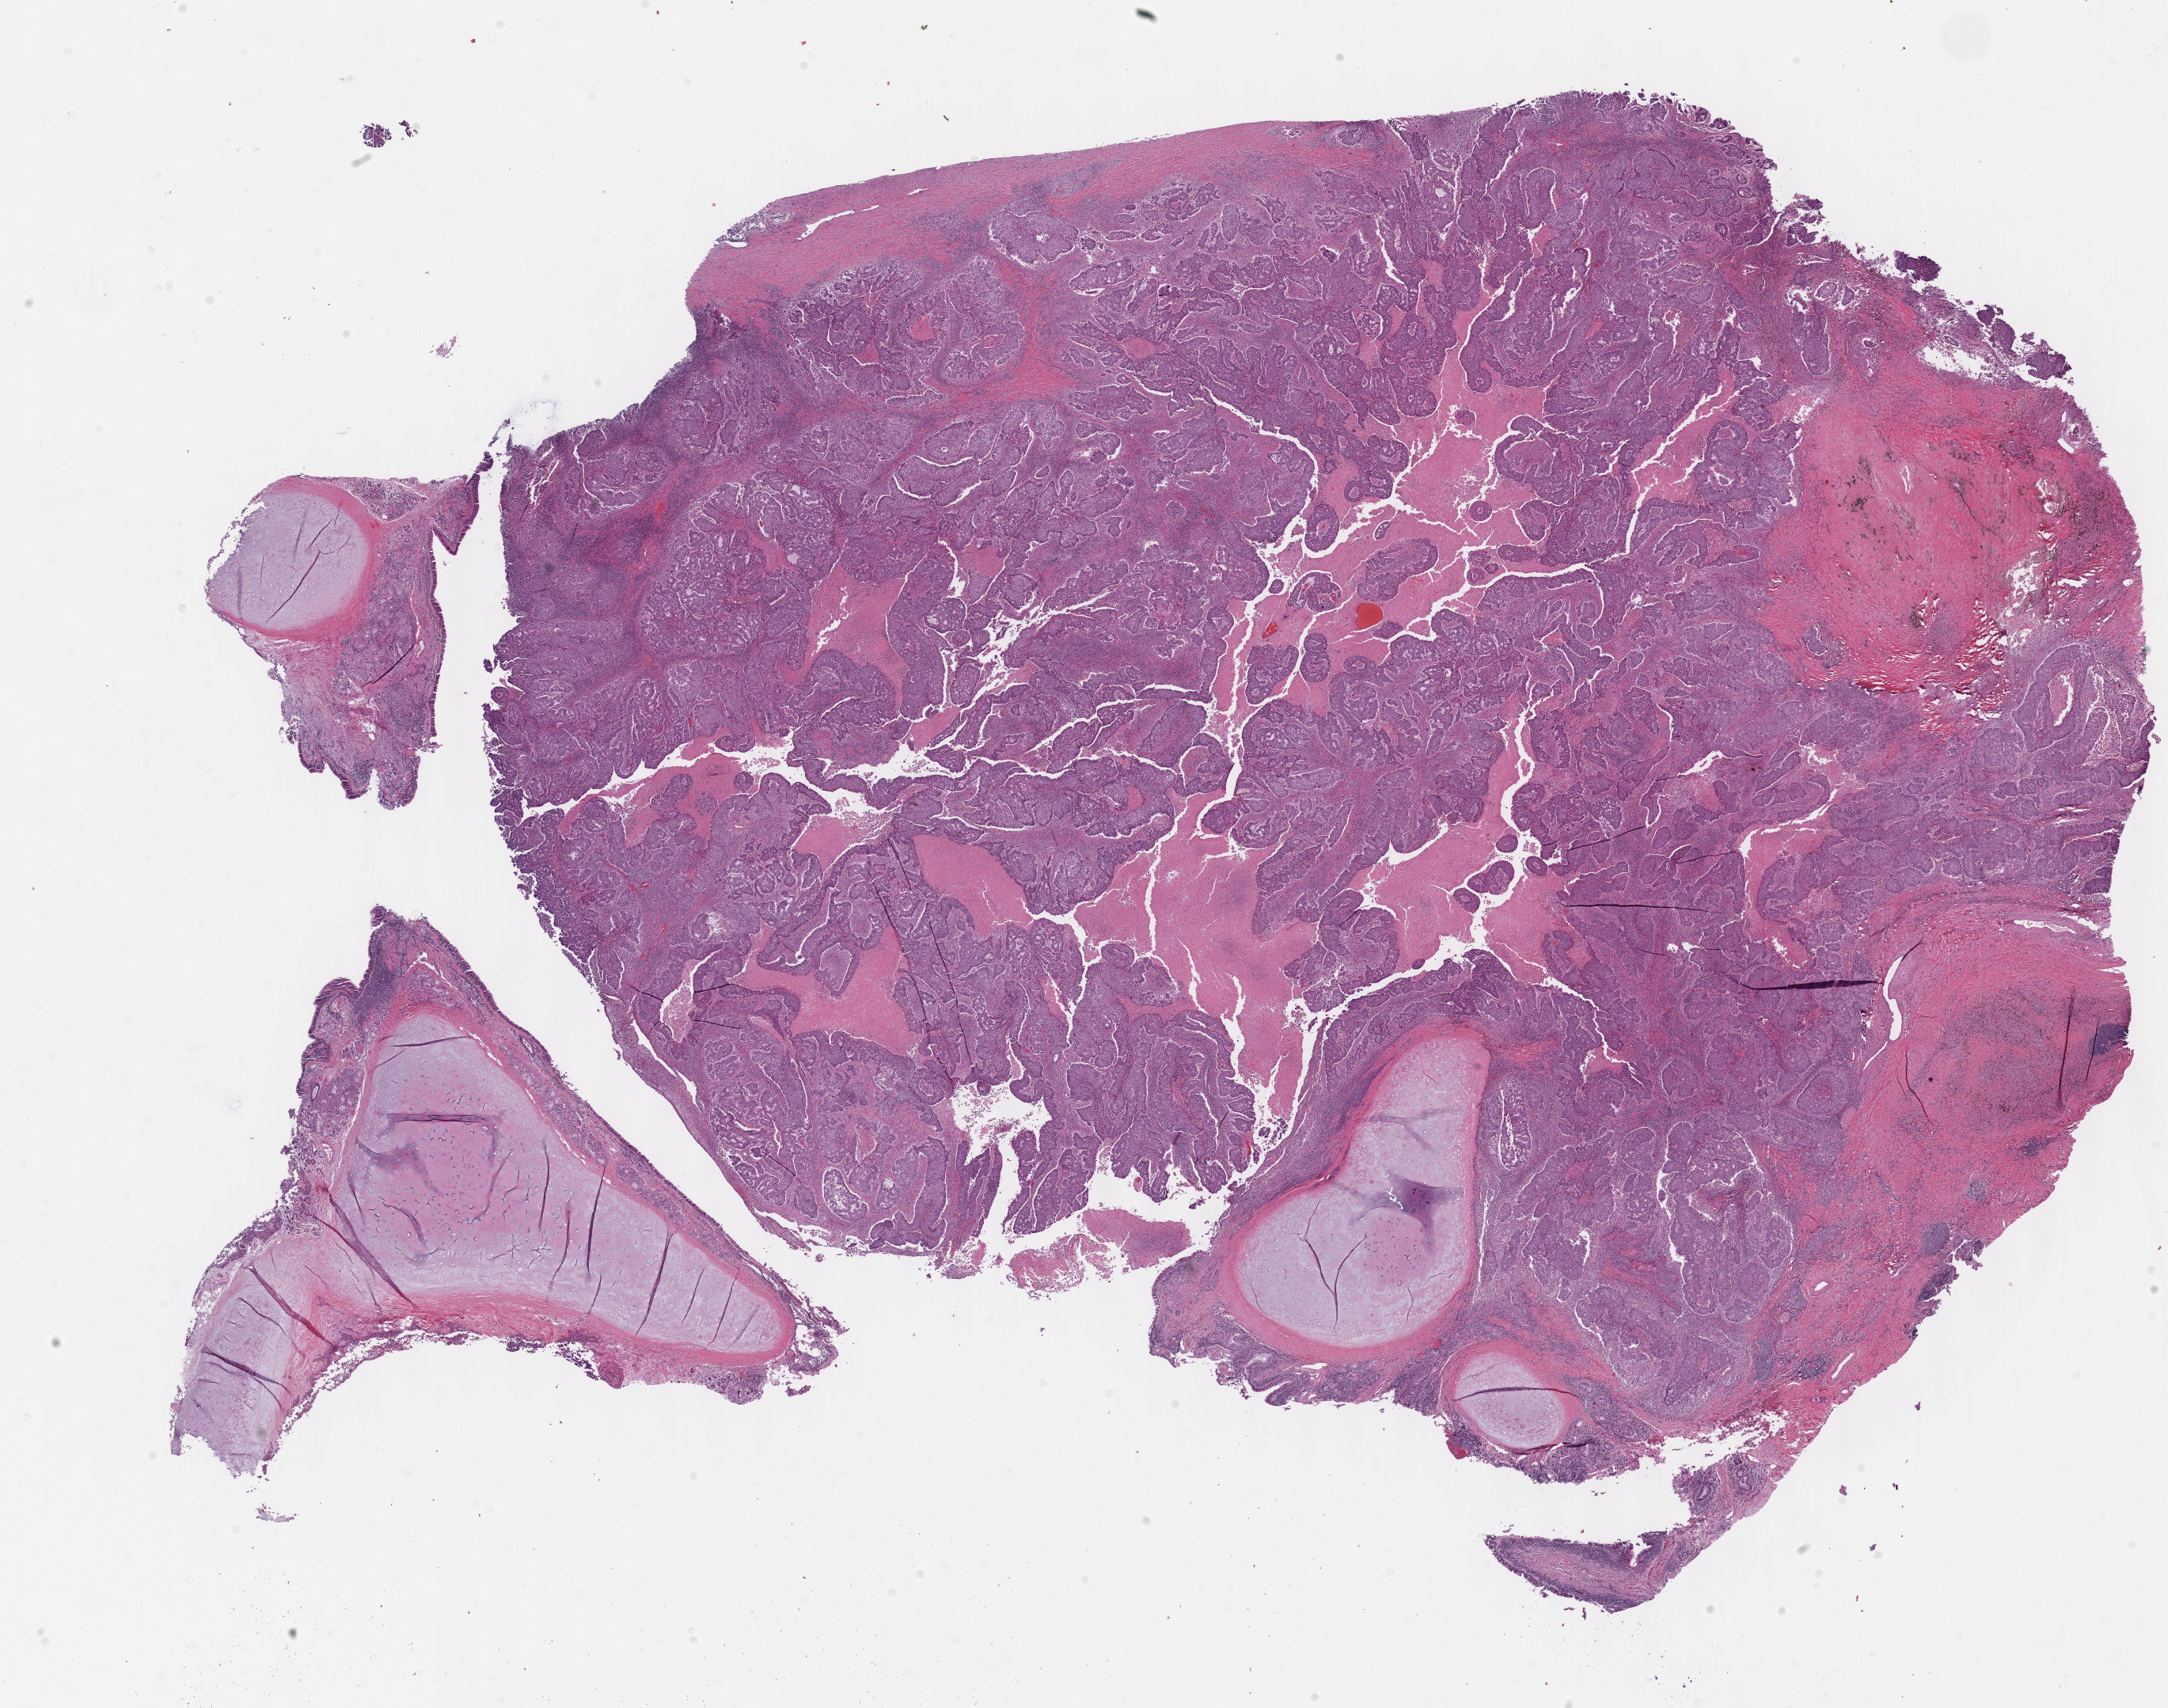
Digitized H&E-stained tissue section (whole slide) — whole scanned area (about 22.1 x 17.4 mm) shown as a low-resolution overview. FFPE section. Sample: primary tumour, lung. Female patient; age at initial diagnosis 73 years.
Diagnosis: Squamous cell carcinoma, NOS (overlapping lesion of lung).